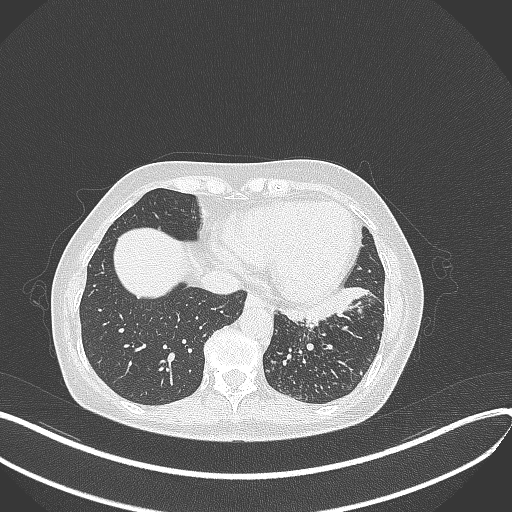
Chest CT, one axial slice. Reconstruction kernel B70f. 100 kVp. Lung window (W 1500 / L -600 HU). 512 × 512 image matrix, field of view 400 × 400 mm. Patient: female, 63 years. From the clinical record (not read from this slice): clinical TNM (as recorded): T1b N0 M0.
Structures marked on this image (rectangle marked by the reading radiologist):
- lung tumour (recorded histology: adenocarcinoma): bounding box [x1, y1, x2, y2] px = [284, 282, 376, 330]